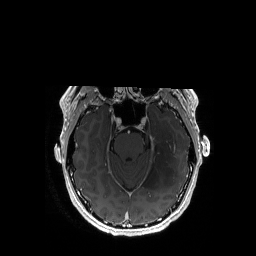
Brain MRI from a brain-tumour surgery series, one axial slice; slice 118 of 192 in the series (ordered by position); T1-weighted post-contrast; 1 mm slice thickness; 256 × 256 image matrix, field of view 256 × 256 mm. From the clinical record (not read from this slice): histopathology: Astrocytoma; WHO grade: 3; IDH mutation: yes.
Outlined on this slice (expert manual segmentation):
- tumour: bounding box [x1, y1, x2, y2] px = [143, 114, 178, 189]